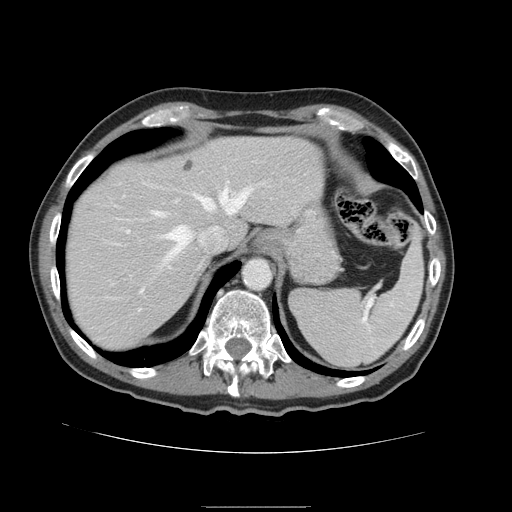
Contrast-enhanced abdominal CT, one axial slice. Position 121 of 168 along the scan axis. 120 kVp. Soft-tissue window (W 400 / L 40 HU). 2.5 mm slice thickness. 512 × 512 image matrix. Male patient, age 74 years. Case-level facts recorded for this patient, not image findings: diagnosis: colorectal cancer liver metastases, imaged before liver resection; multiple liver metastases: no; largest metastasis: 14.5 cm.
Outlined on this slice (manually delineated by an expert):
- hepatic veins: box from (x=140, y=182) to (x=269, y=293) px
- liver: (x=65, y=138)–(x=325, y=351)
- planned liver remnant (the part of the liver to remain after resection): (x=65, y=137)–(x=324, y=351)